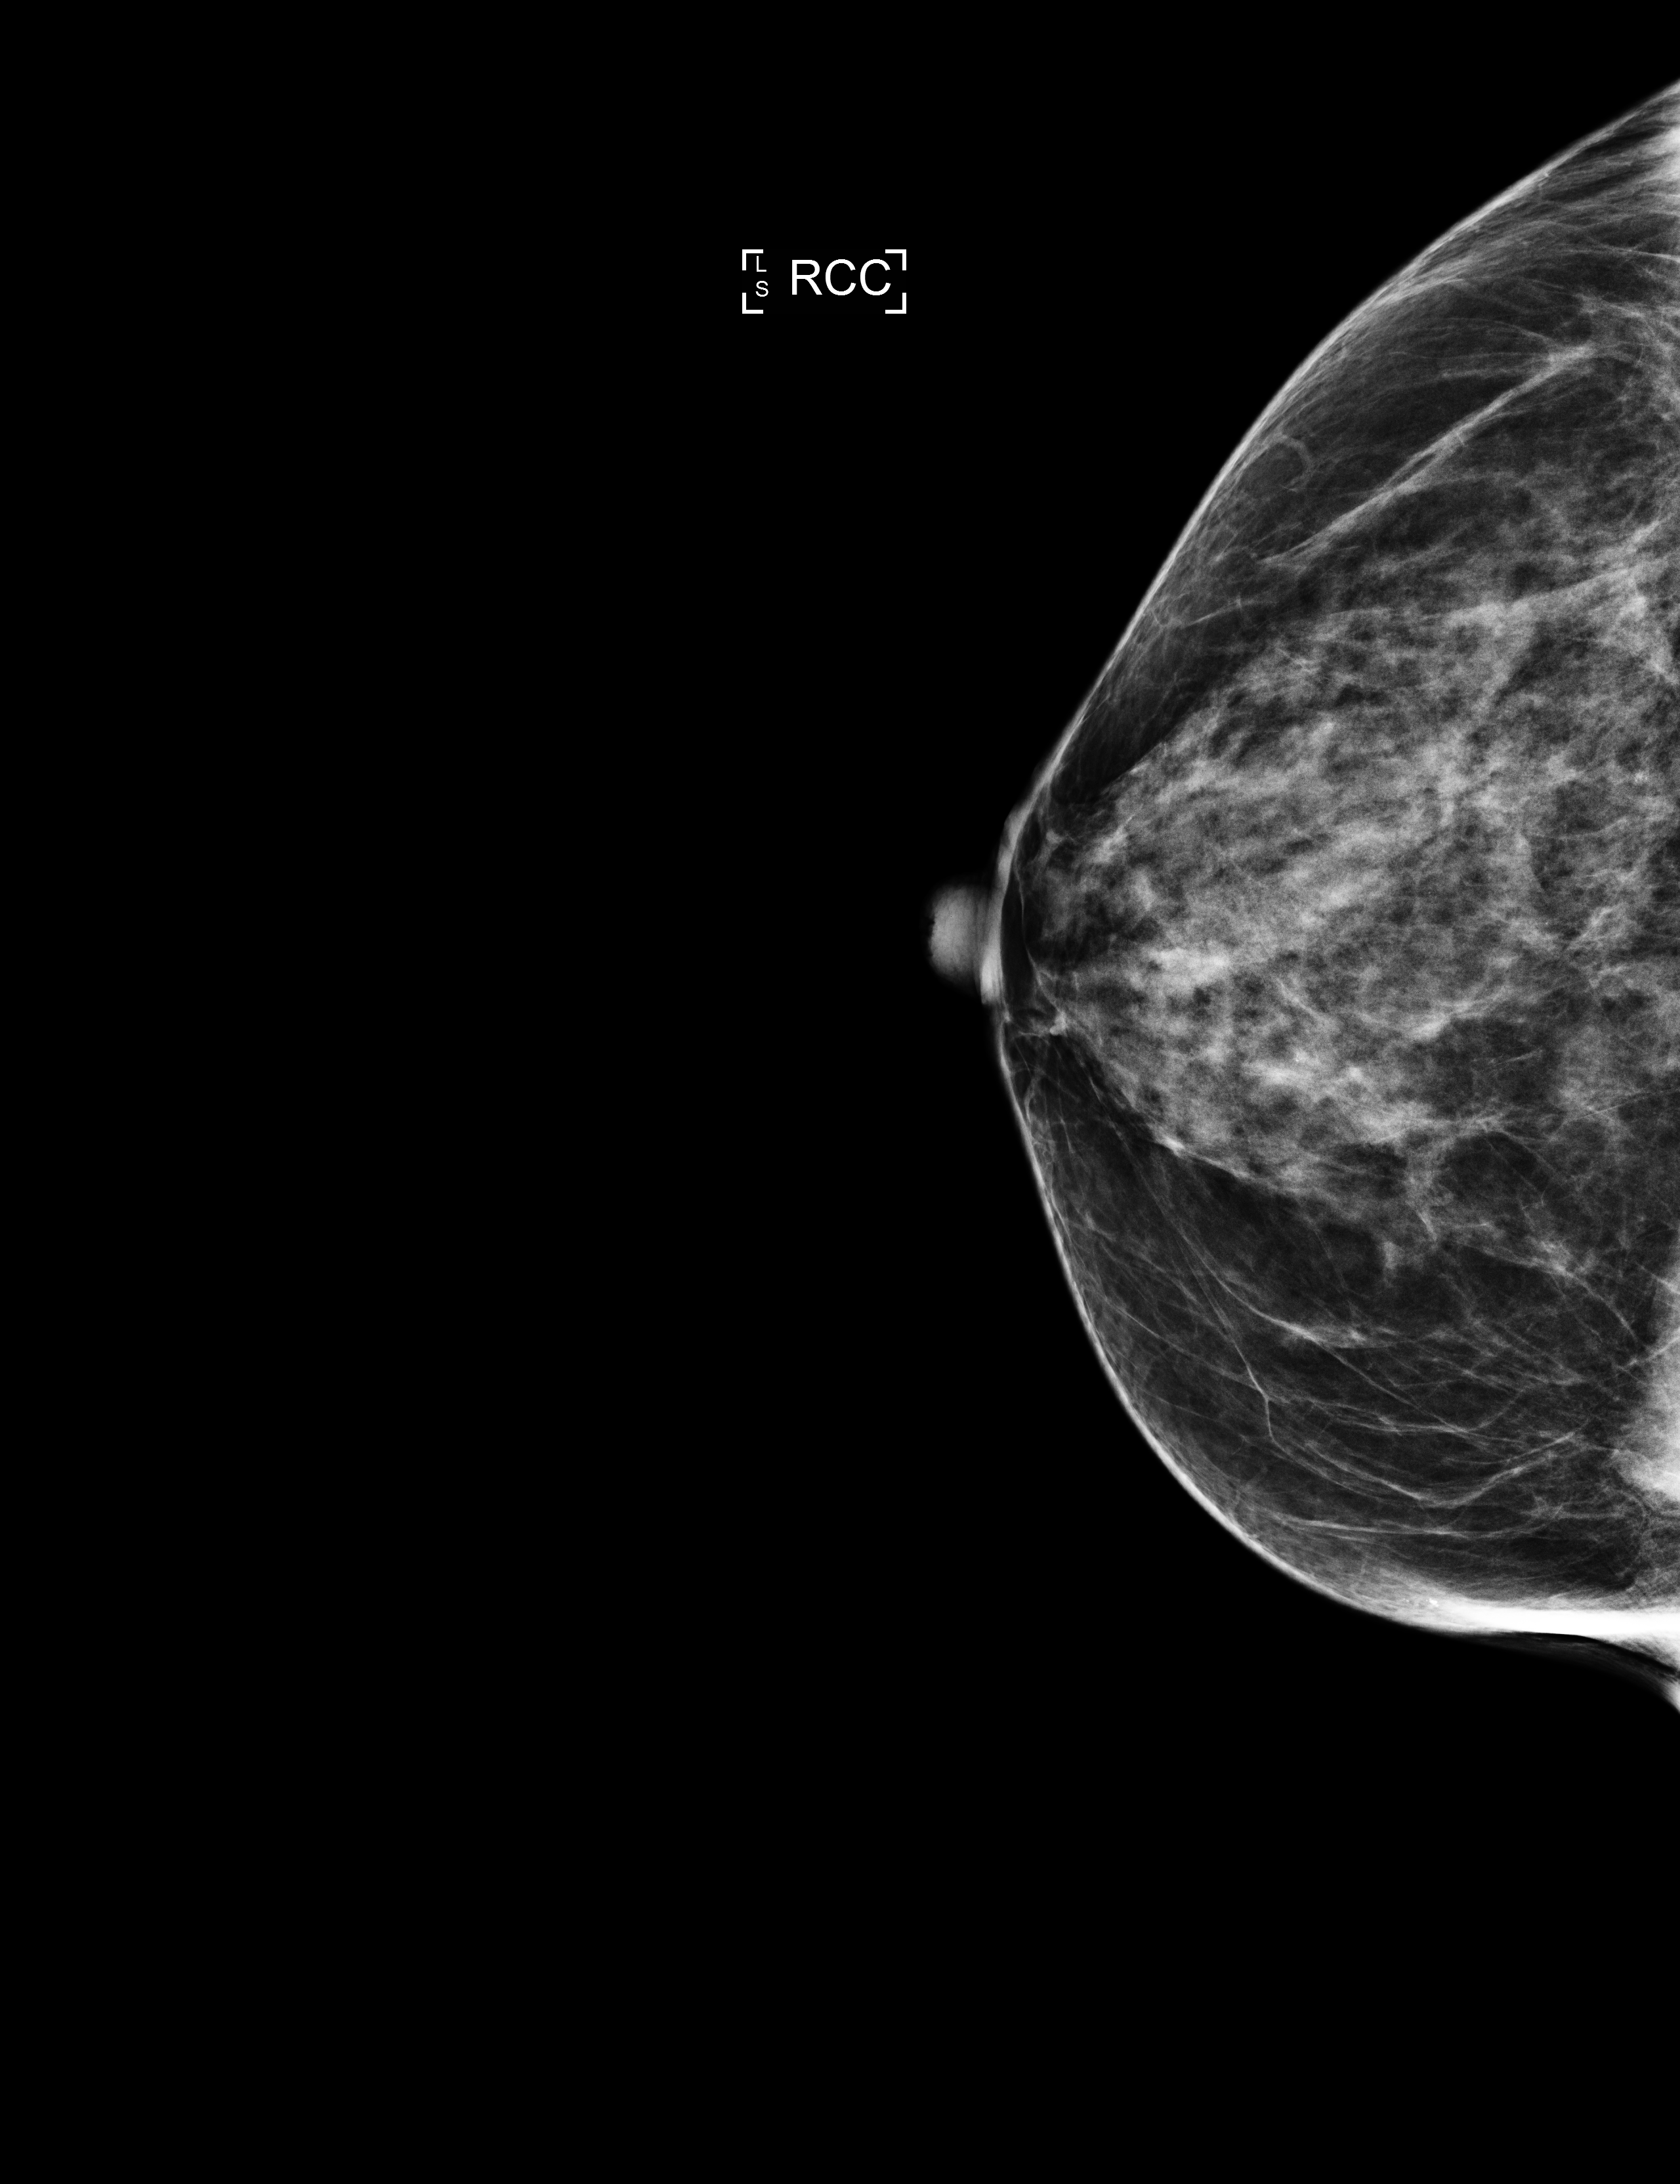
Annual screening mammography examination, system: Selenia Dimensions. Patient aged 61 years (female).
Image type: full-field digital mammogram. Breast: right. Projection: CC view.